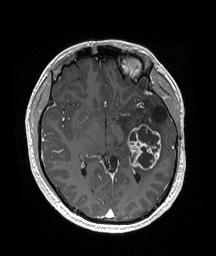
Brain MRI from a brain-tumour surgery series, one axial slice. Position 98 of 192 along the scan axis. T1-weighted post-contrast. 216 × 256 image matrix, field of view 211 × 250 mm. From the clinical record (not read from this slice): histopathology: Glioneuronal tumor; WHO grade: 2.
Structures marked on this image (manually delineated by an expert):
- previous resection cavity: bounding box (x1, y1, x2, y2) in pixels: (153, 107, 168, 123)
- tumour: (128, 124, 161, 170)